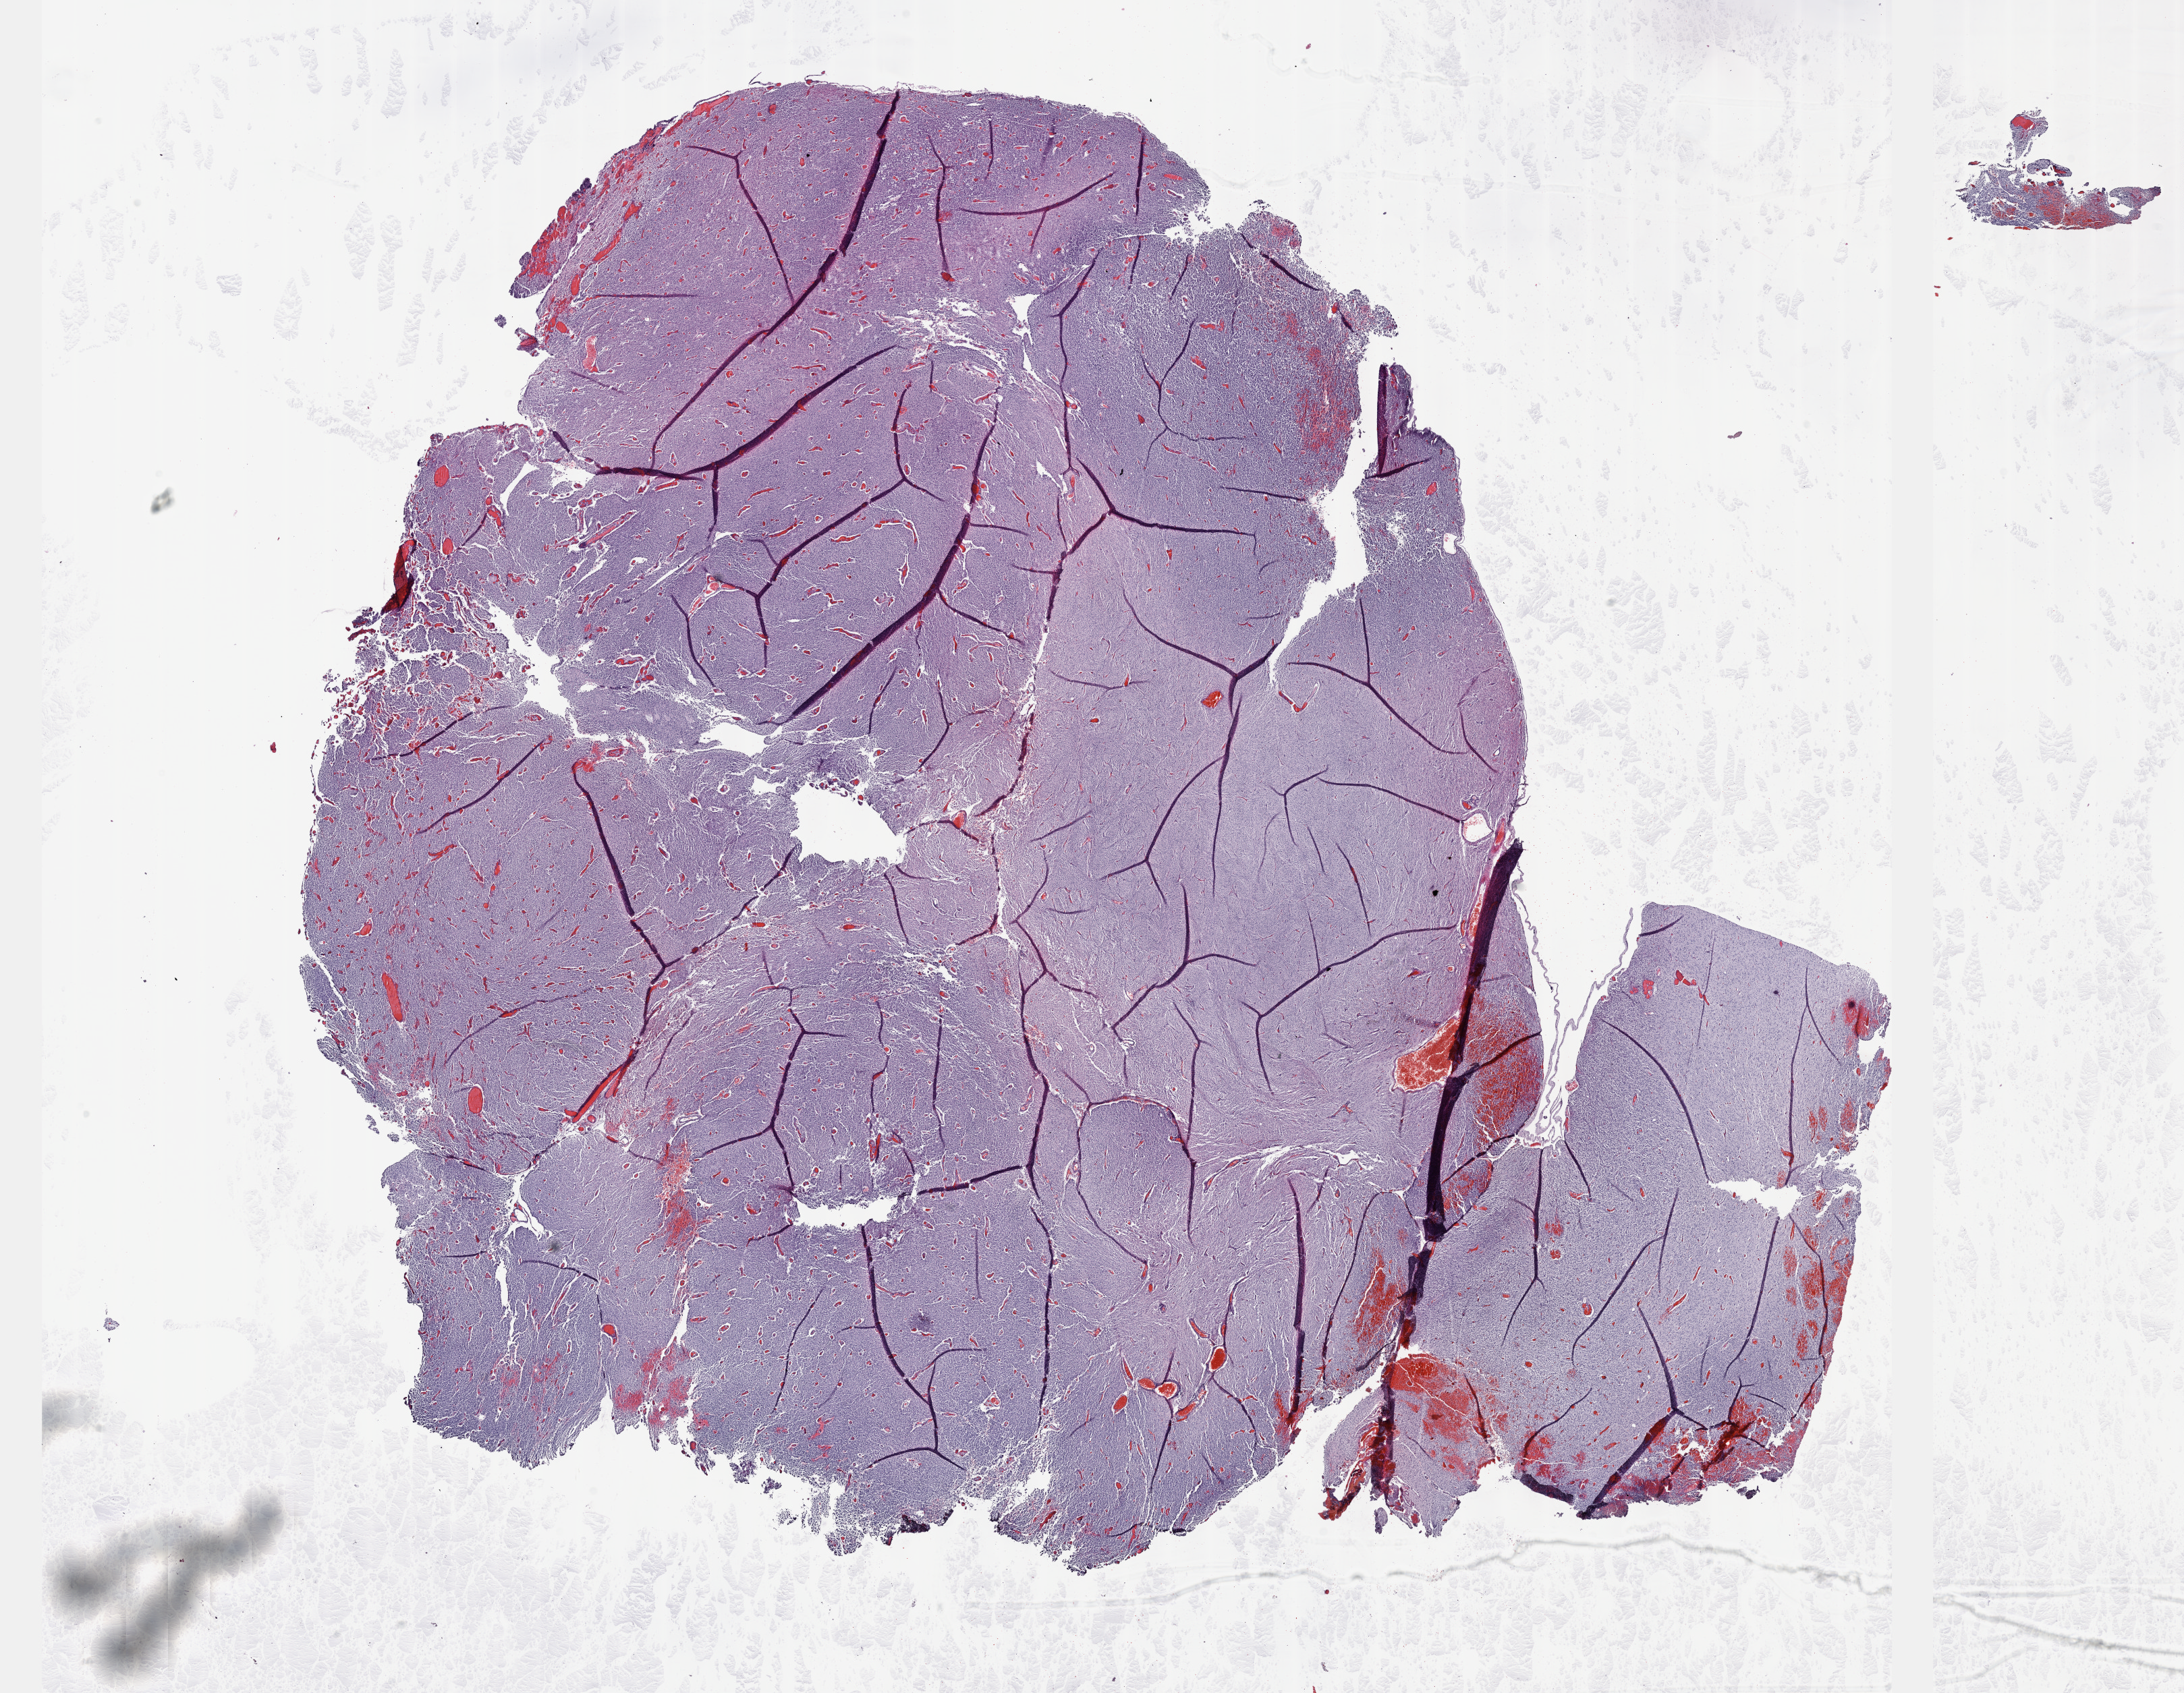
Digitized H&E-stained tissue section (whole slide), shown as a low-resolution overview of the whole scanned area (about 26.2 x 20.3 mm), formalin-fixed paraffin-embedded (FFPE) diagnostic section, brain, primary tumour sample. Male patient; age at initial diagnosis 44 years. Histologic grade: G3 (poorly differentiated).
Diagnosis: Mixed glioma (cerebrum).